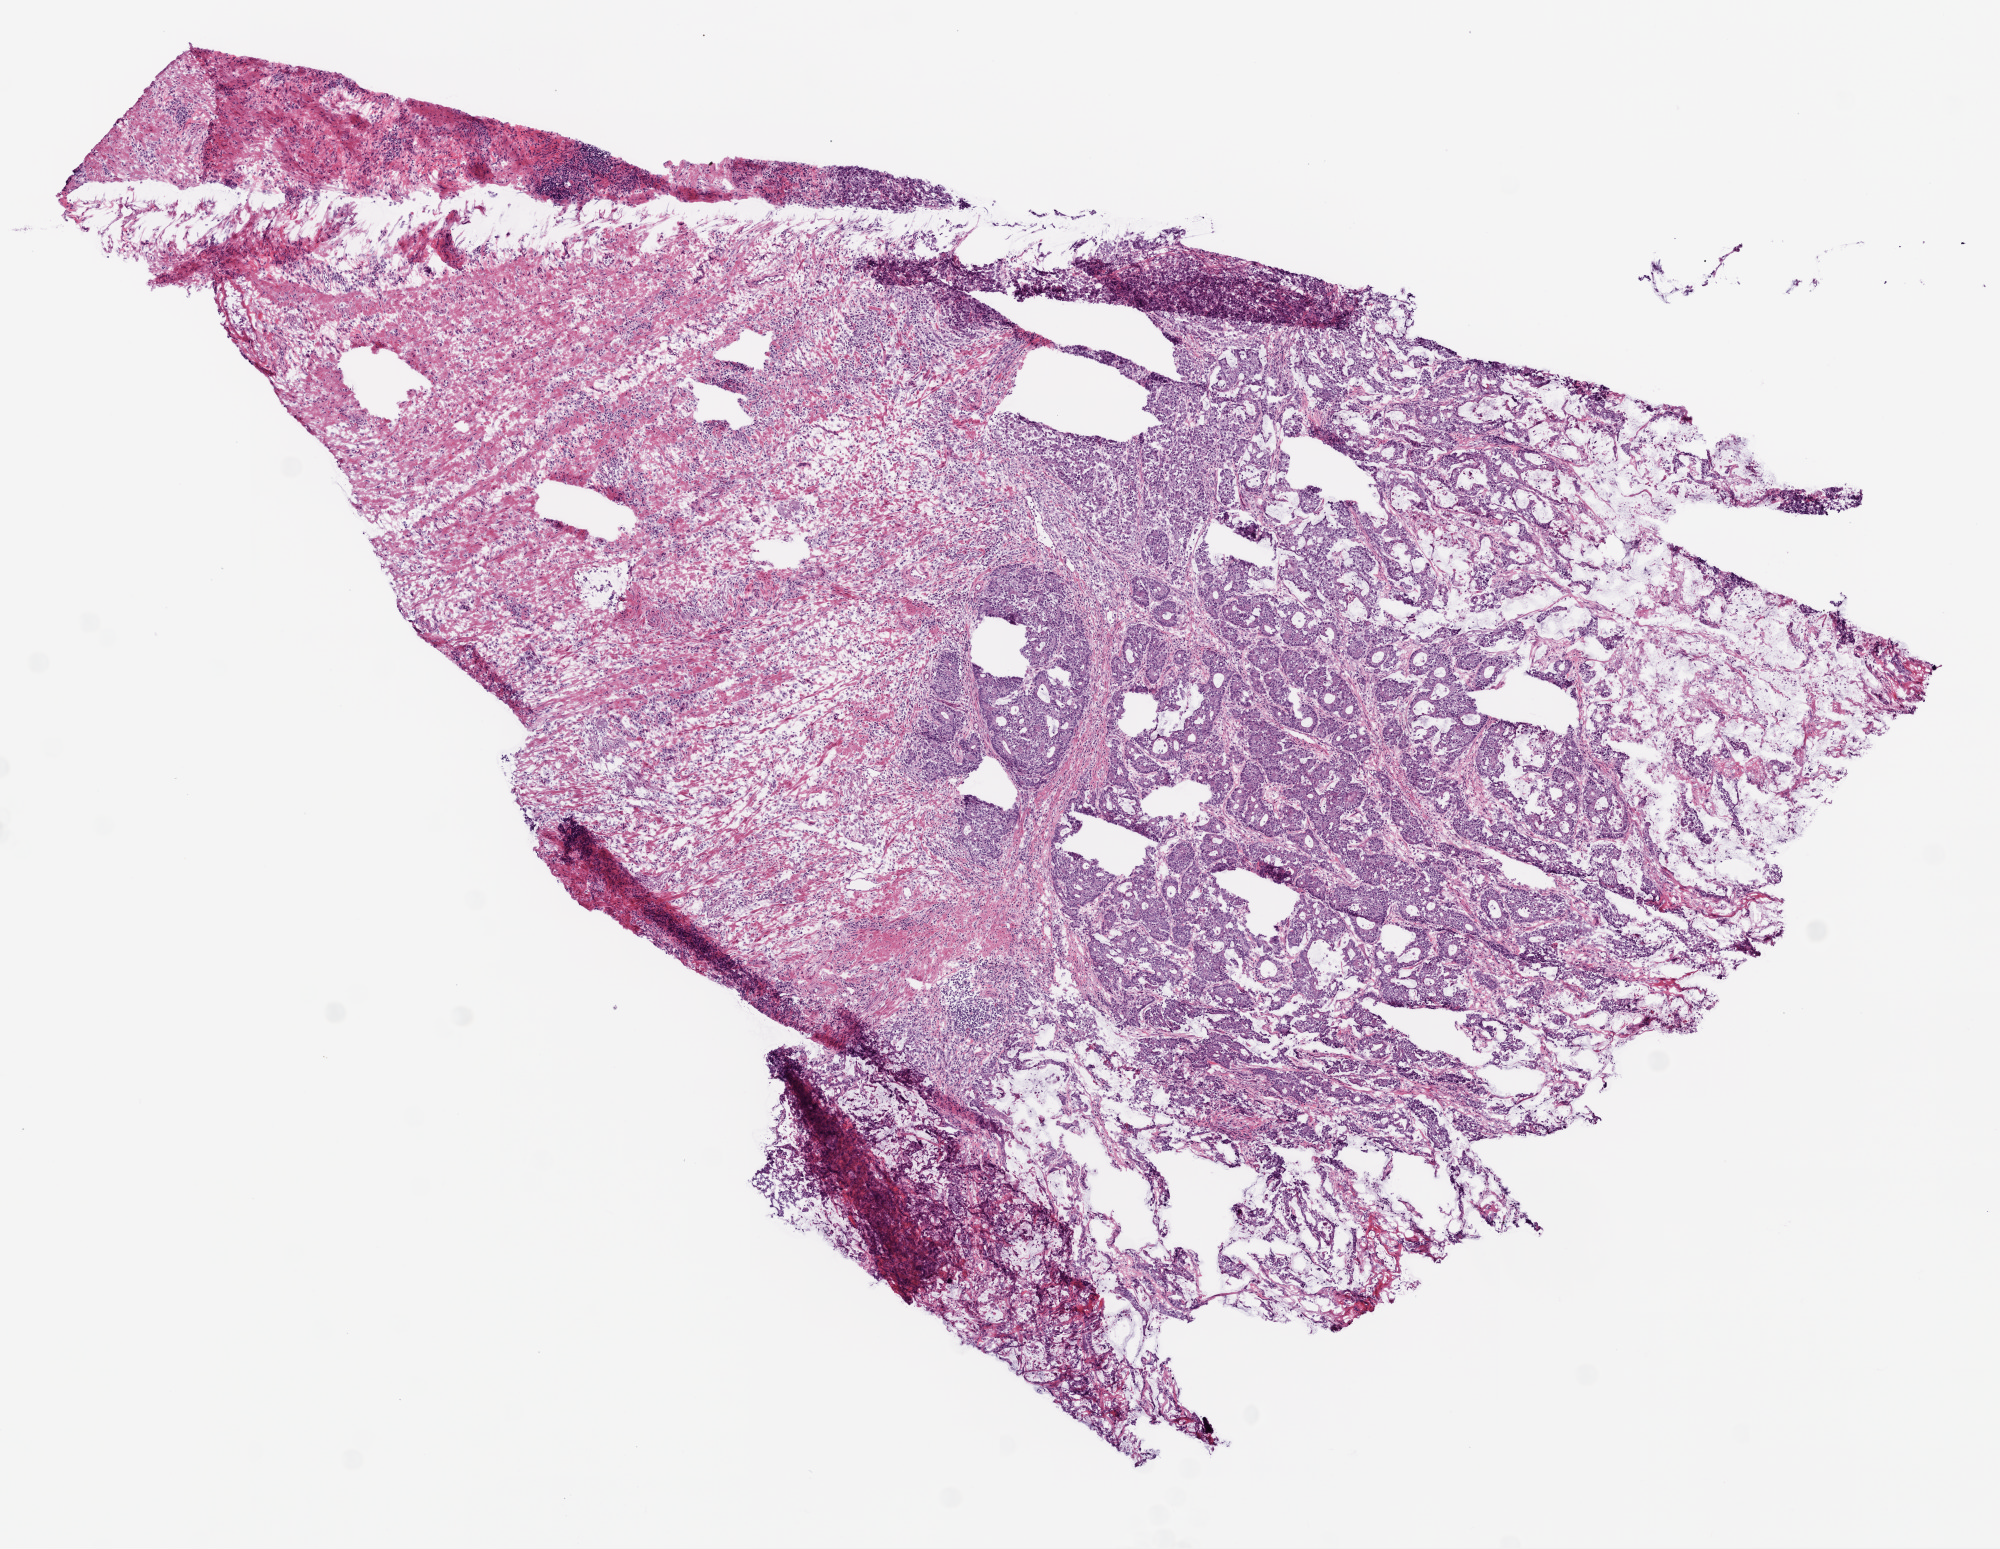
Whole-slide histology image, H&E, whole scanned area (about 8.0 x 6.2 mm, acquisition: 20x scan) shown as a low-resolution overview. Frozen section from the top of the tissue portion. Colon, primary tumour sample. Female patient. Composition of this section per pathologist review: tumour cells 52%, tumour nuclei 65%, normal cells 0%, stromal cells 40%, necrosis 8%.
TNM: T3 N1 M0. Histologic diagnosis: Mucinous adenocarcinoma (ascending colon). Lymph nodes positive (case pathology): 3 of 19 examined. AJCC pathologic stage: IIIB.